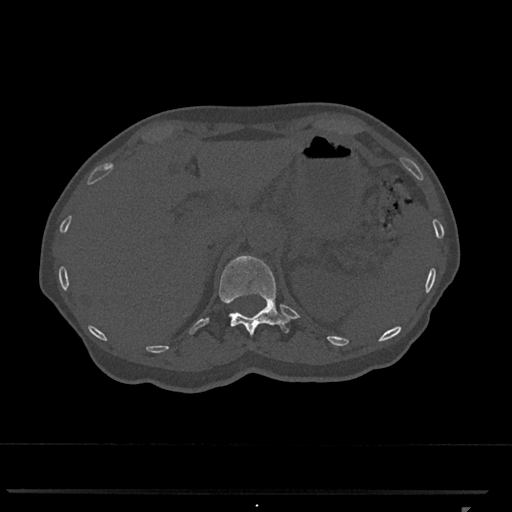
CT including the spine, one axial slice; slice 458 of 793 in the series (ordered by position); reconstruction kernel Br40s/3; 120 kVp; bone window (W 1800 / L 400 HU); 0.5 mm slice thickness; 512 × 512 image matrix, field of view 380 × 380 mm. Female patient, age 62 years. From the clinical record (not read from this slice): primary cancer: renal.
Structures marked on this image (semi-automatic segmentation, software-assisted and operator-edited):
- T12 vertebra: bounding box <219,255,291,336> (left, top, right, bottom; pixels)